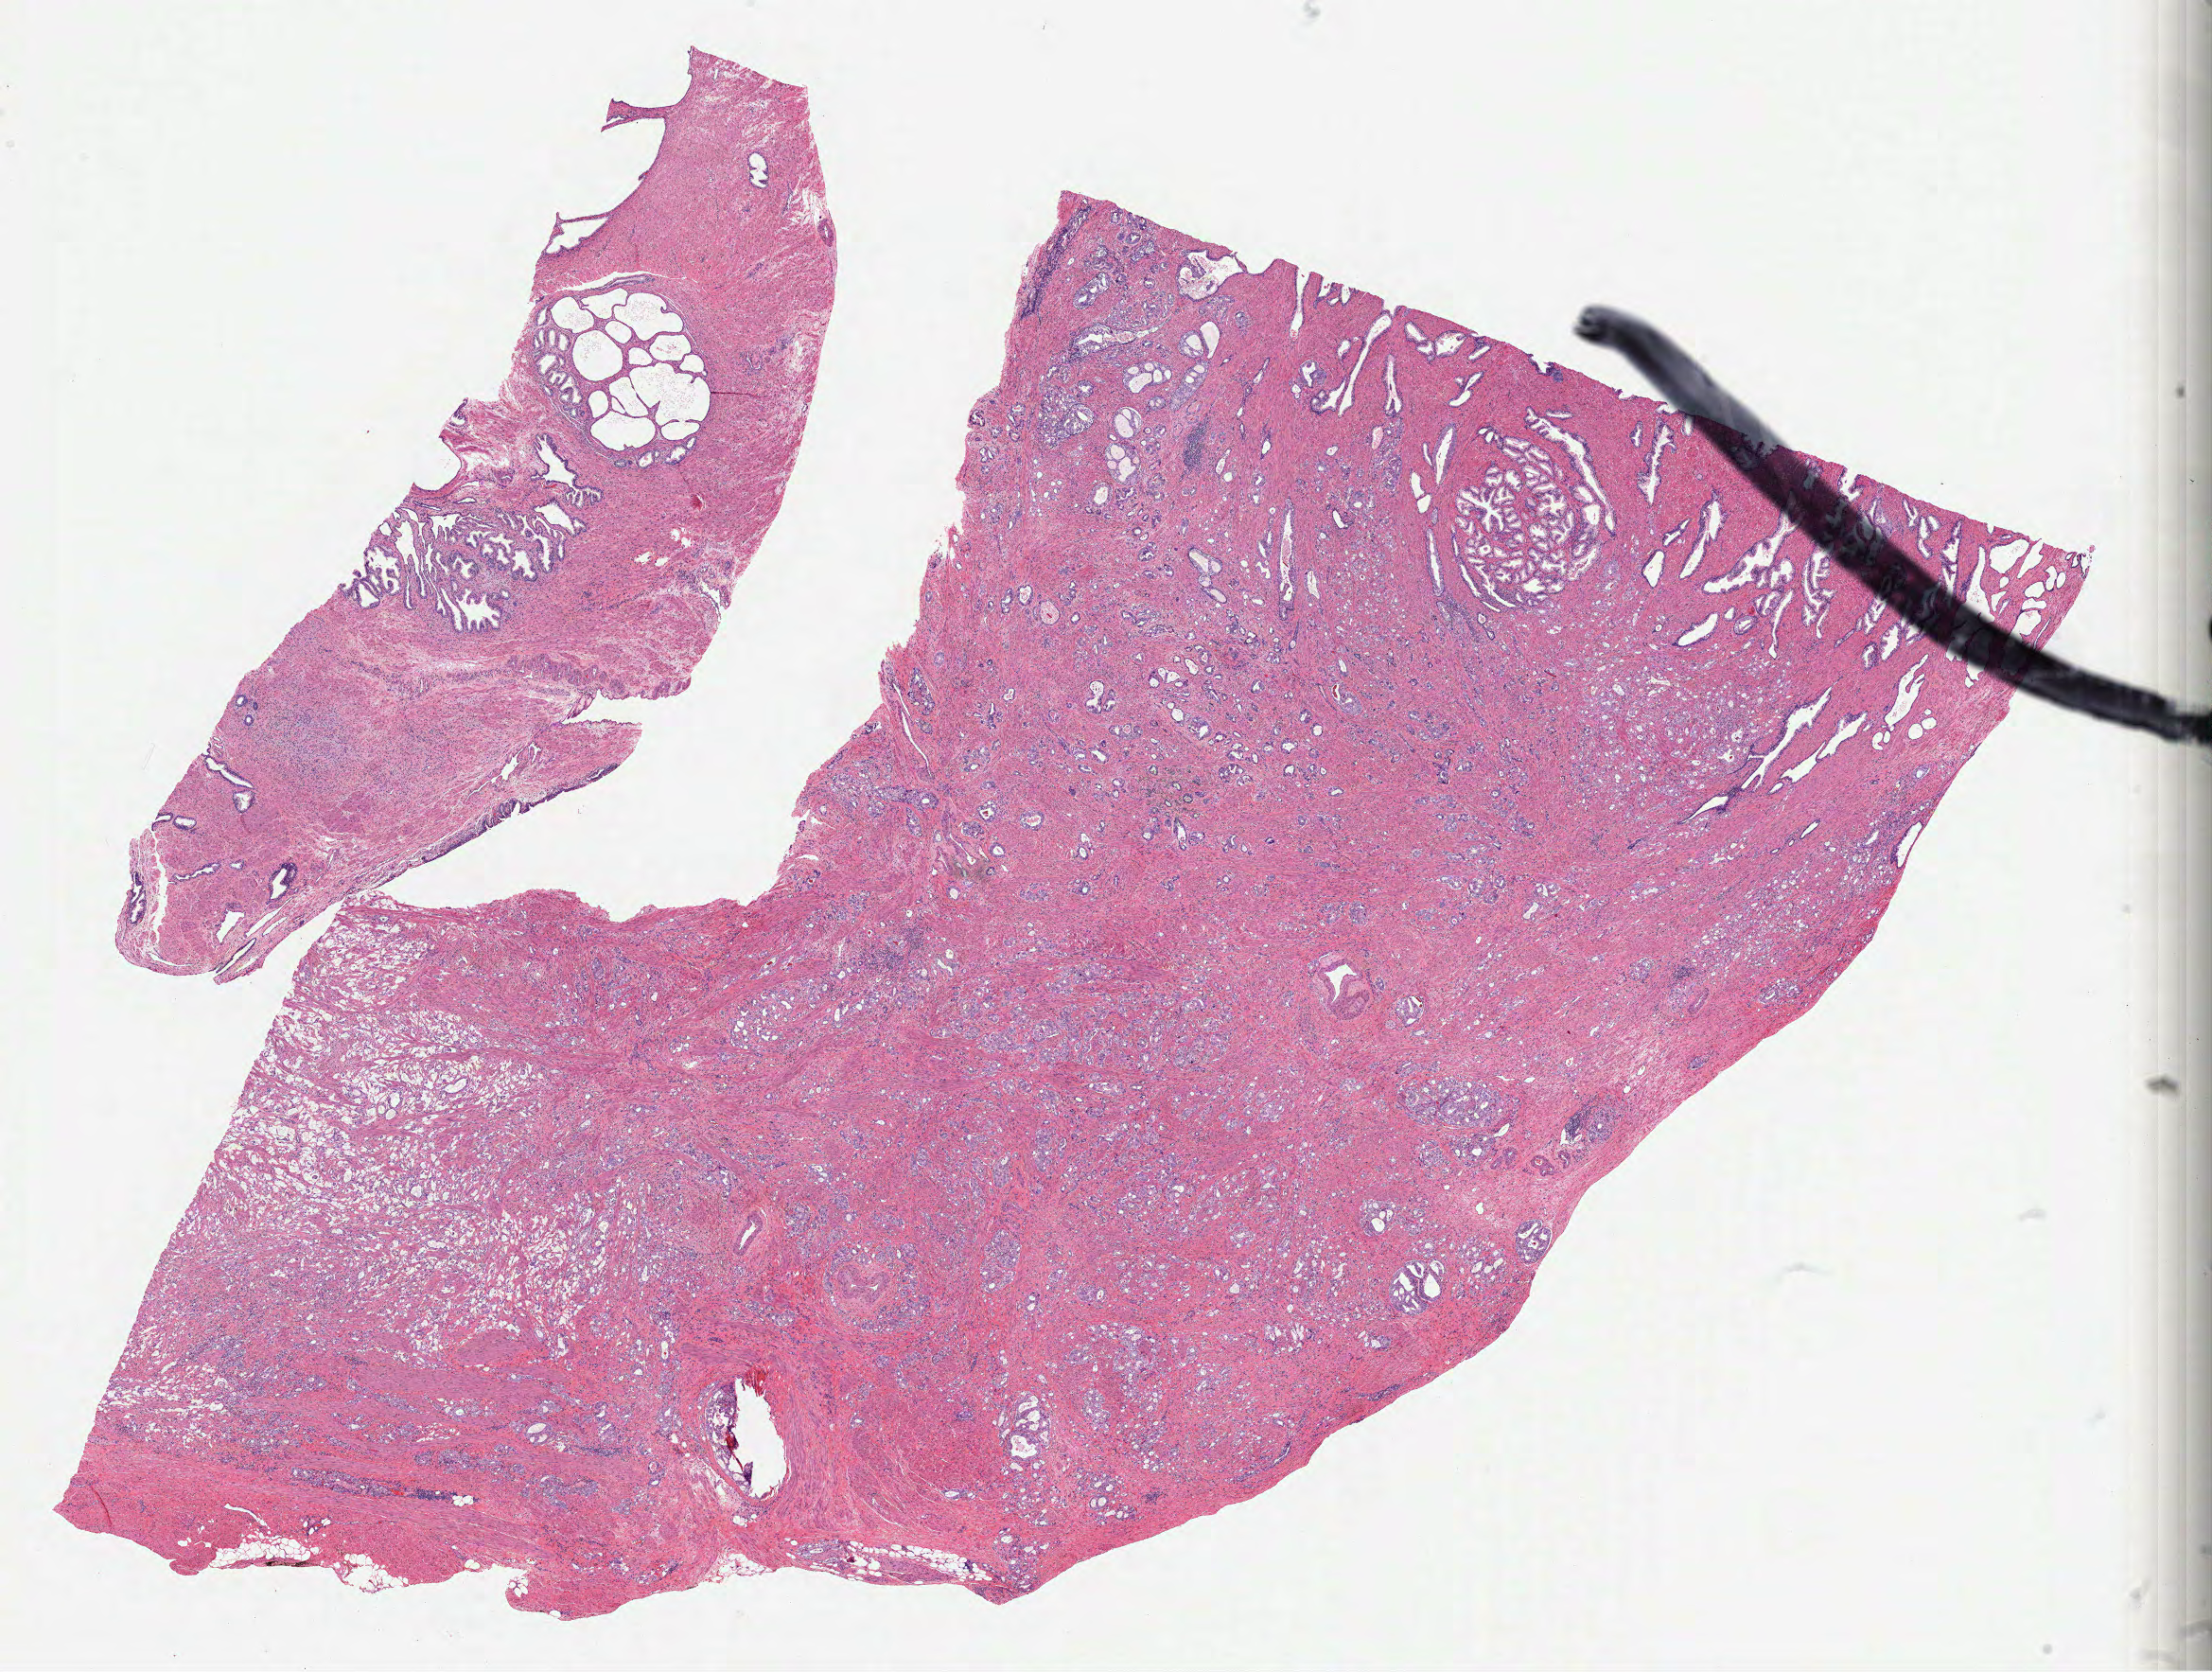
Digitized Hematoxylin and eosin (H&E) stained tissue section (whole slide), whole scanned area (about 18.9 x 14.3 mm, acquisition: 40x scan) shown as a low-resolution overview. Formalin-fixed paraffin-embedded (FFPE) diagnostic section. Primary tumour sample from the prostate. Male patient; age at initial diagnosis 66 years. Gleason score: 9 (4+5).
- histologic diagnosis: Acinar cell carcinoma (prostate gland)
- laterality: bilateral
- lymph nodes positive (case pathology): 0 of 12 examined